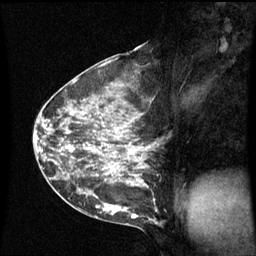
Breast MRI (dynamic contrast-enhanced), one sagittal slice. Slice 29 of 60 in the series (ordered by position). Dynamic contrast-enhanced series, image 2 of 3 at this slice position (ordered by acquisition). 1.5 T. TE 4.2 ms, TR 8.9 ms. 256 × 256 image matrix. Patient: female, 42 years. From the clinical record (not read from this slice): setting: breast cancer imaged before/during neoadjuvant chemotherapy; receptor status: HER2-positive.
Structures marked on this image (semi-automatic segmentation, software-assisted and operator-edited):
- analysis volume of interest (the breast-tissue region the enhancement analysis was run in; not a lesion): bounding box <62,93,156,210> (left, top, right, bottom; pixels)
- tumour enhancement mask (voxels above the 70 % enhancement threshold inside the analysis volume of interest): <69,128,137,177>